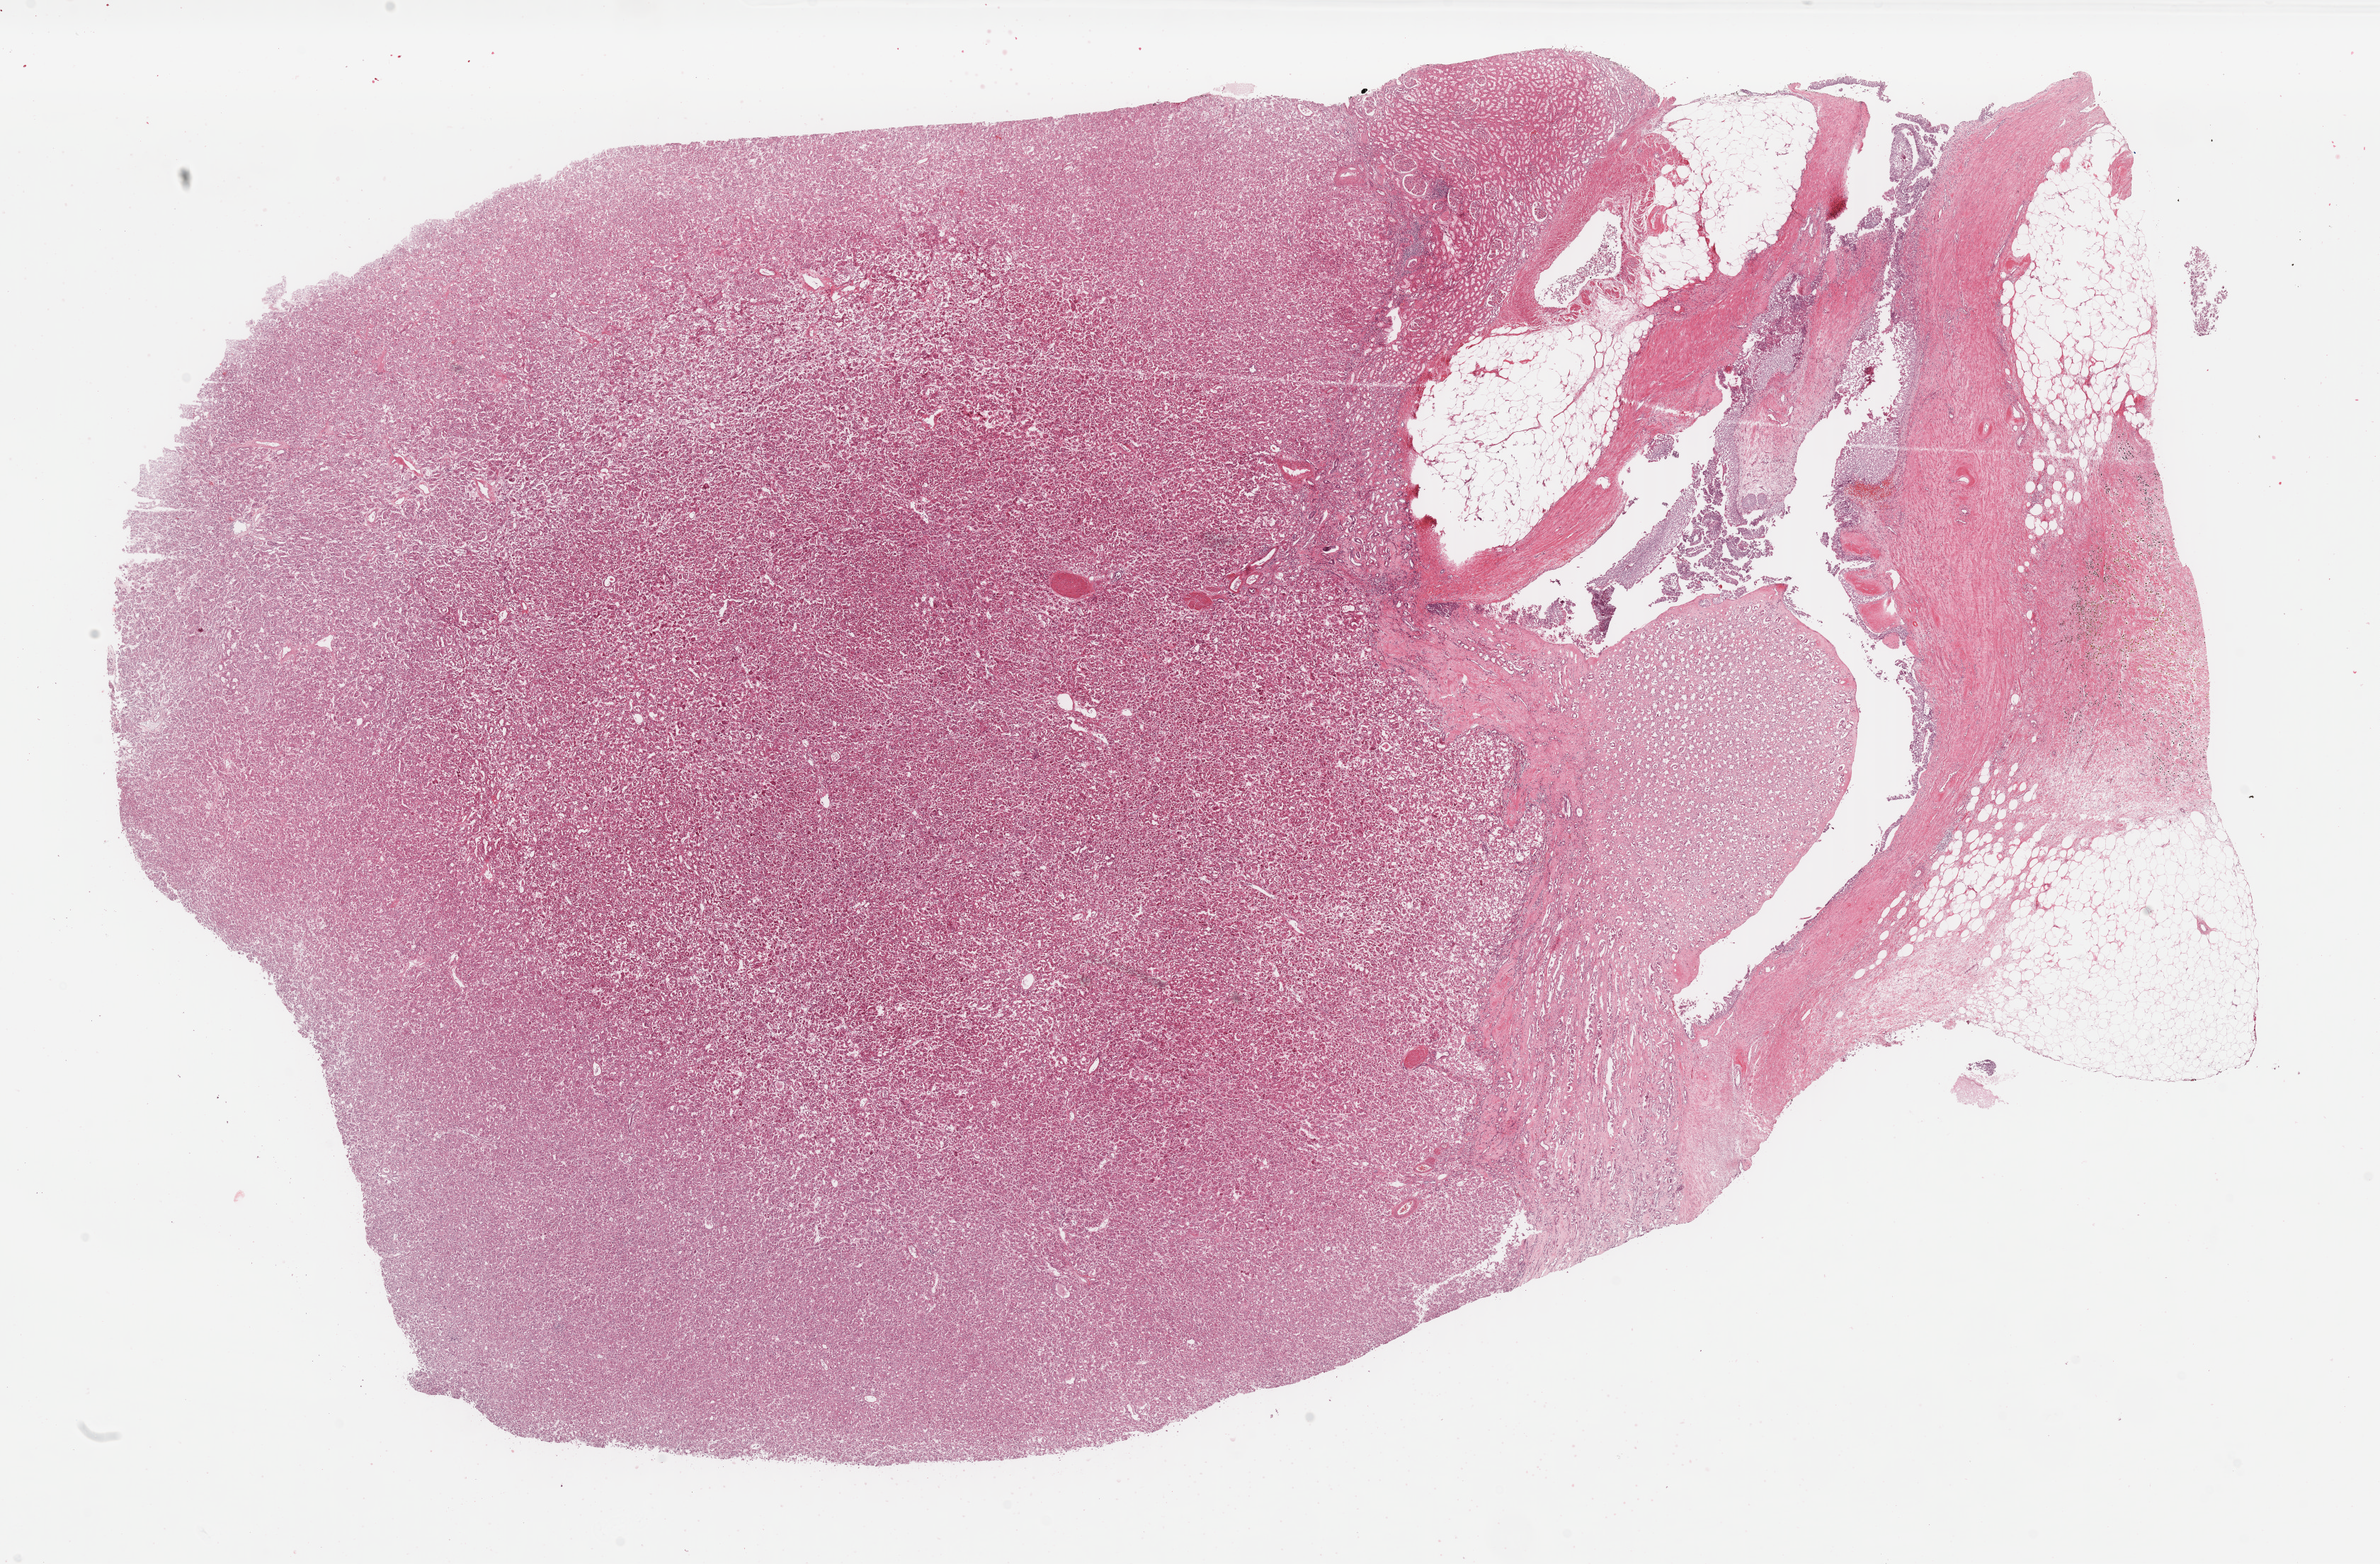
Whole-slide histology image, H&E-stained, low-resolution overview of the scanned area, about 26.6 x 17.5 mm (acquisition: 40x scan). FFPE section. Primary tumour sample from the kidney. Patient: male, age at initial diagnosis 58 years. Composition of this section per pathologist review: tumour cells 70%, tumour nuclei 70%, normal cells 5%, stromal cells 25%, necrosis 0%. Inflammatory infiltration, as recorded: lymphocyte infiltration 3%, monocyte infiltration 1%, neutrophil infiltration 1%.
• AJCC pathologic stage: I (6th edition)
• diagnosis: Renal cell carcinoma, chromophobe type